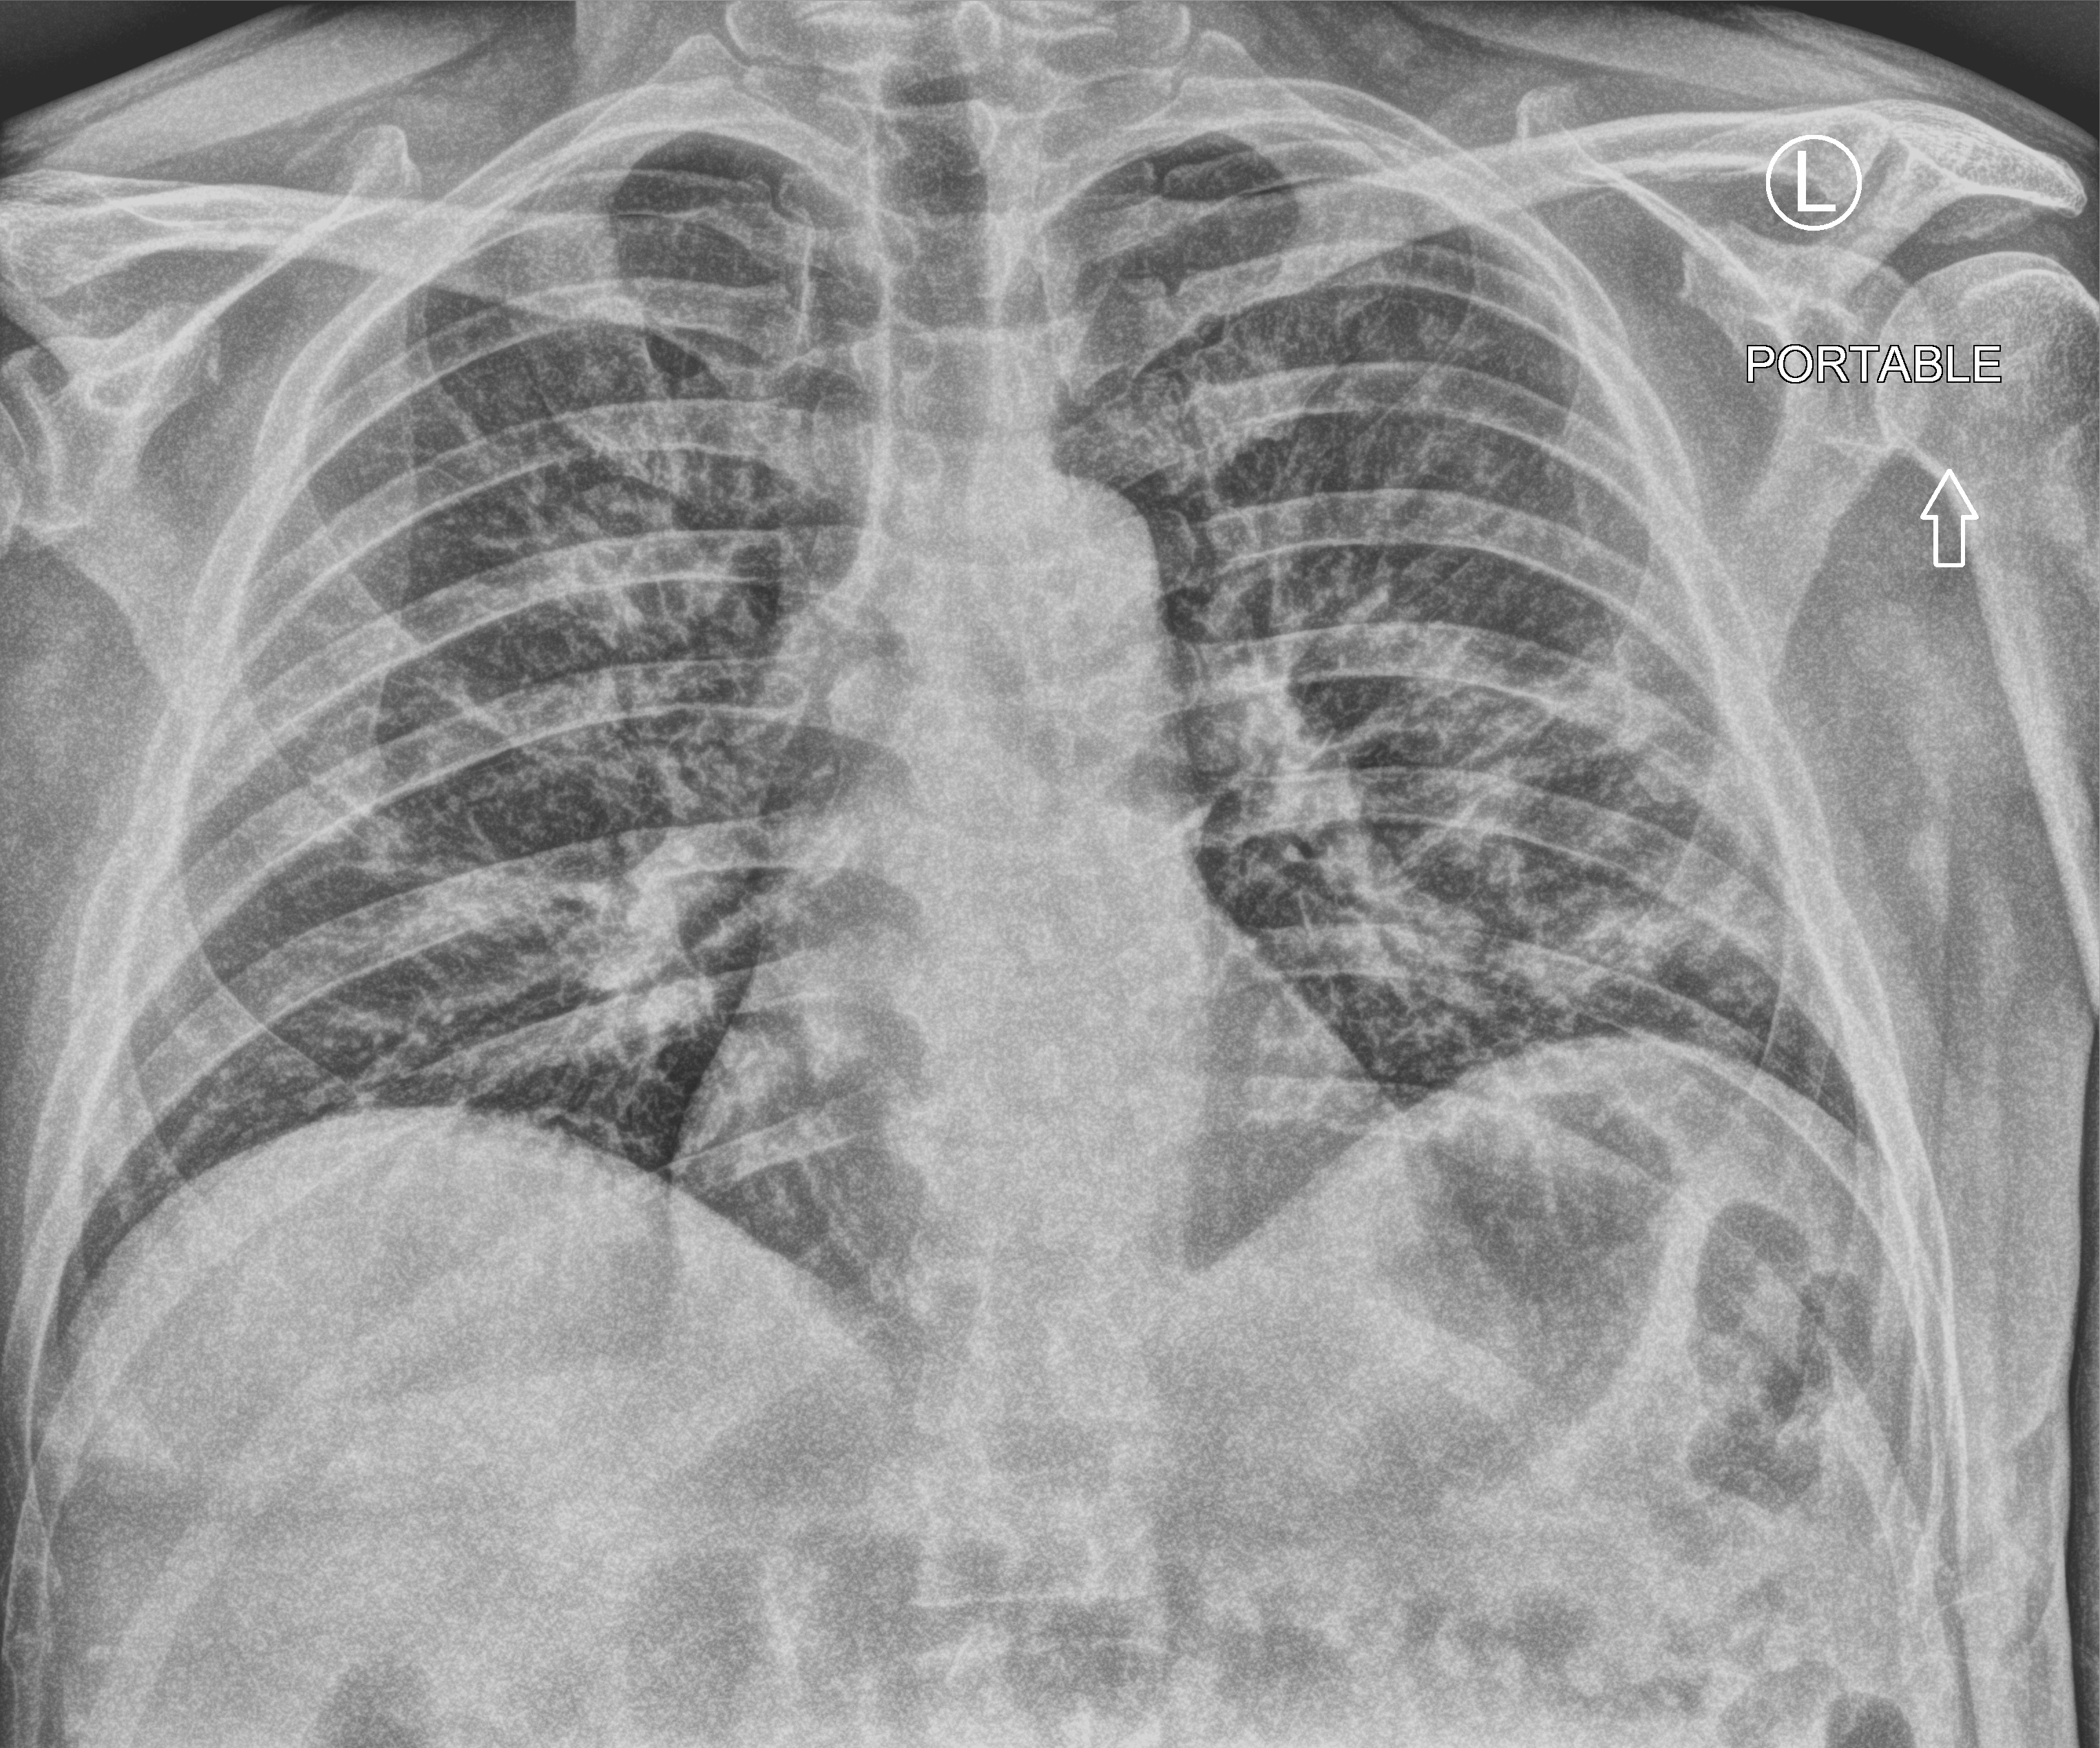
Chest X-ray (portable); anteroposterior (AP) projection. Male patient hospitalised with COVID-19, age 18–59 years.
Admission-level facts for this patient (not findings on this image; timing relative to this image not recorded):
- admitted to intensive care during this hospital stay: no
- hypertension (admission record): no
- mechanically ventilated during this hospital stay: no